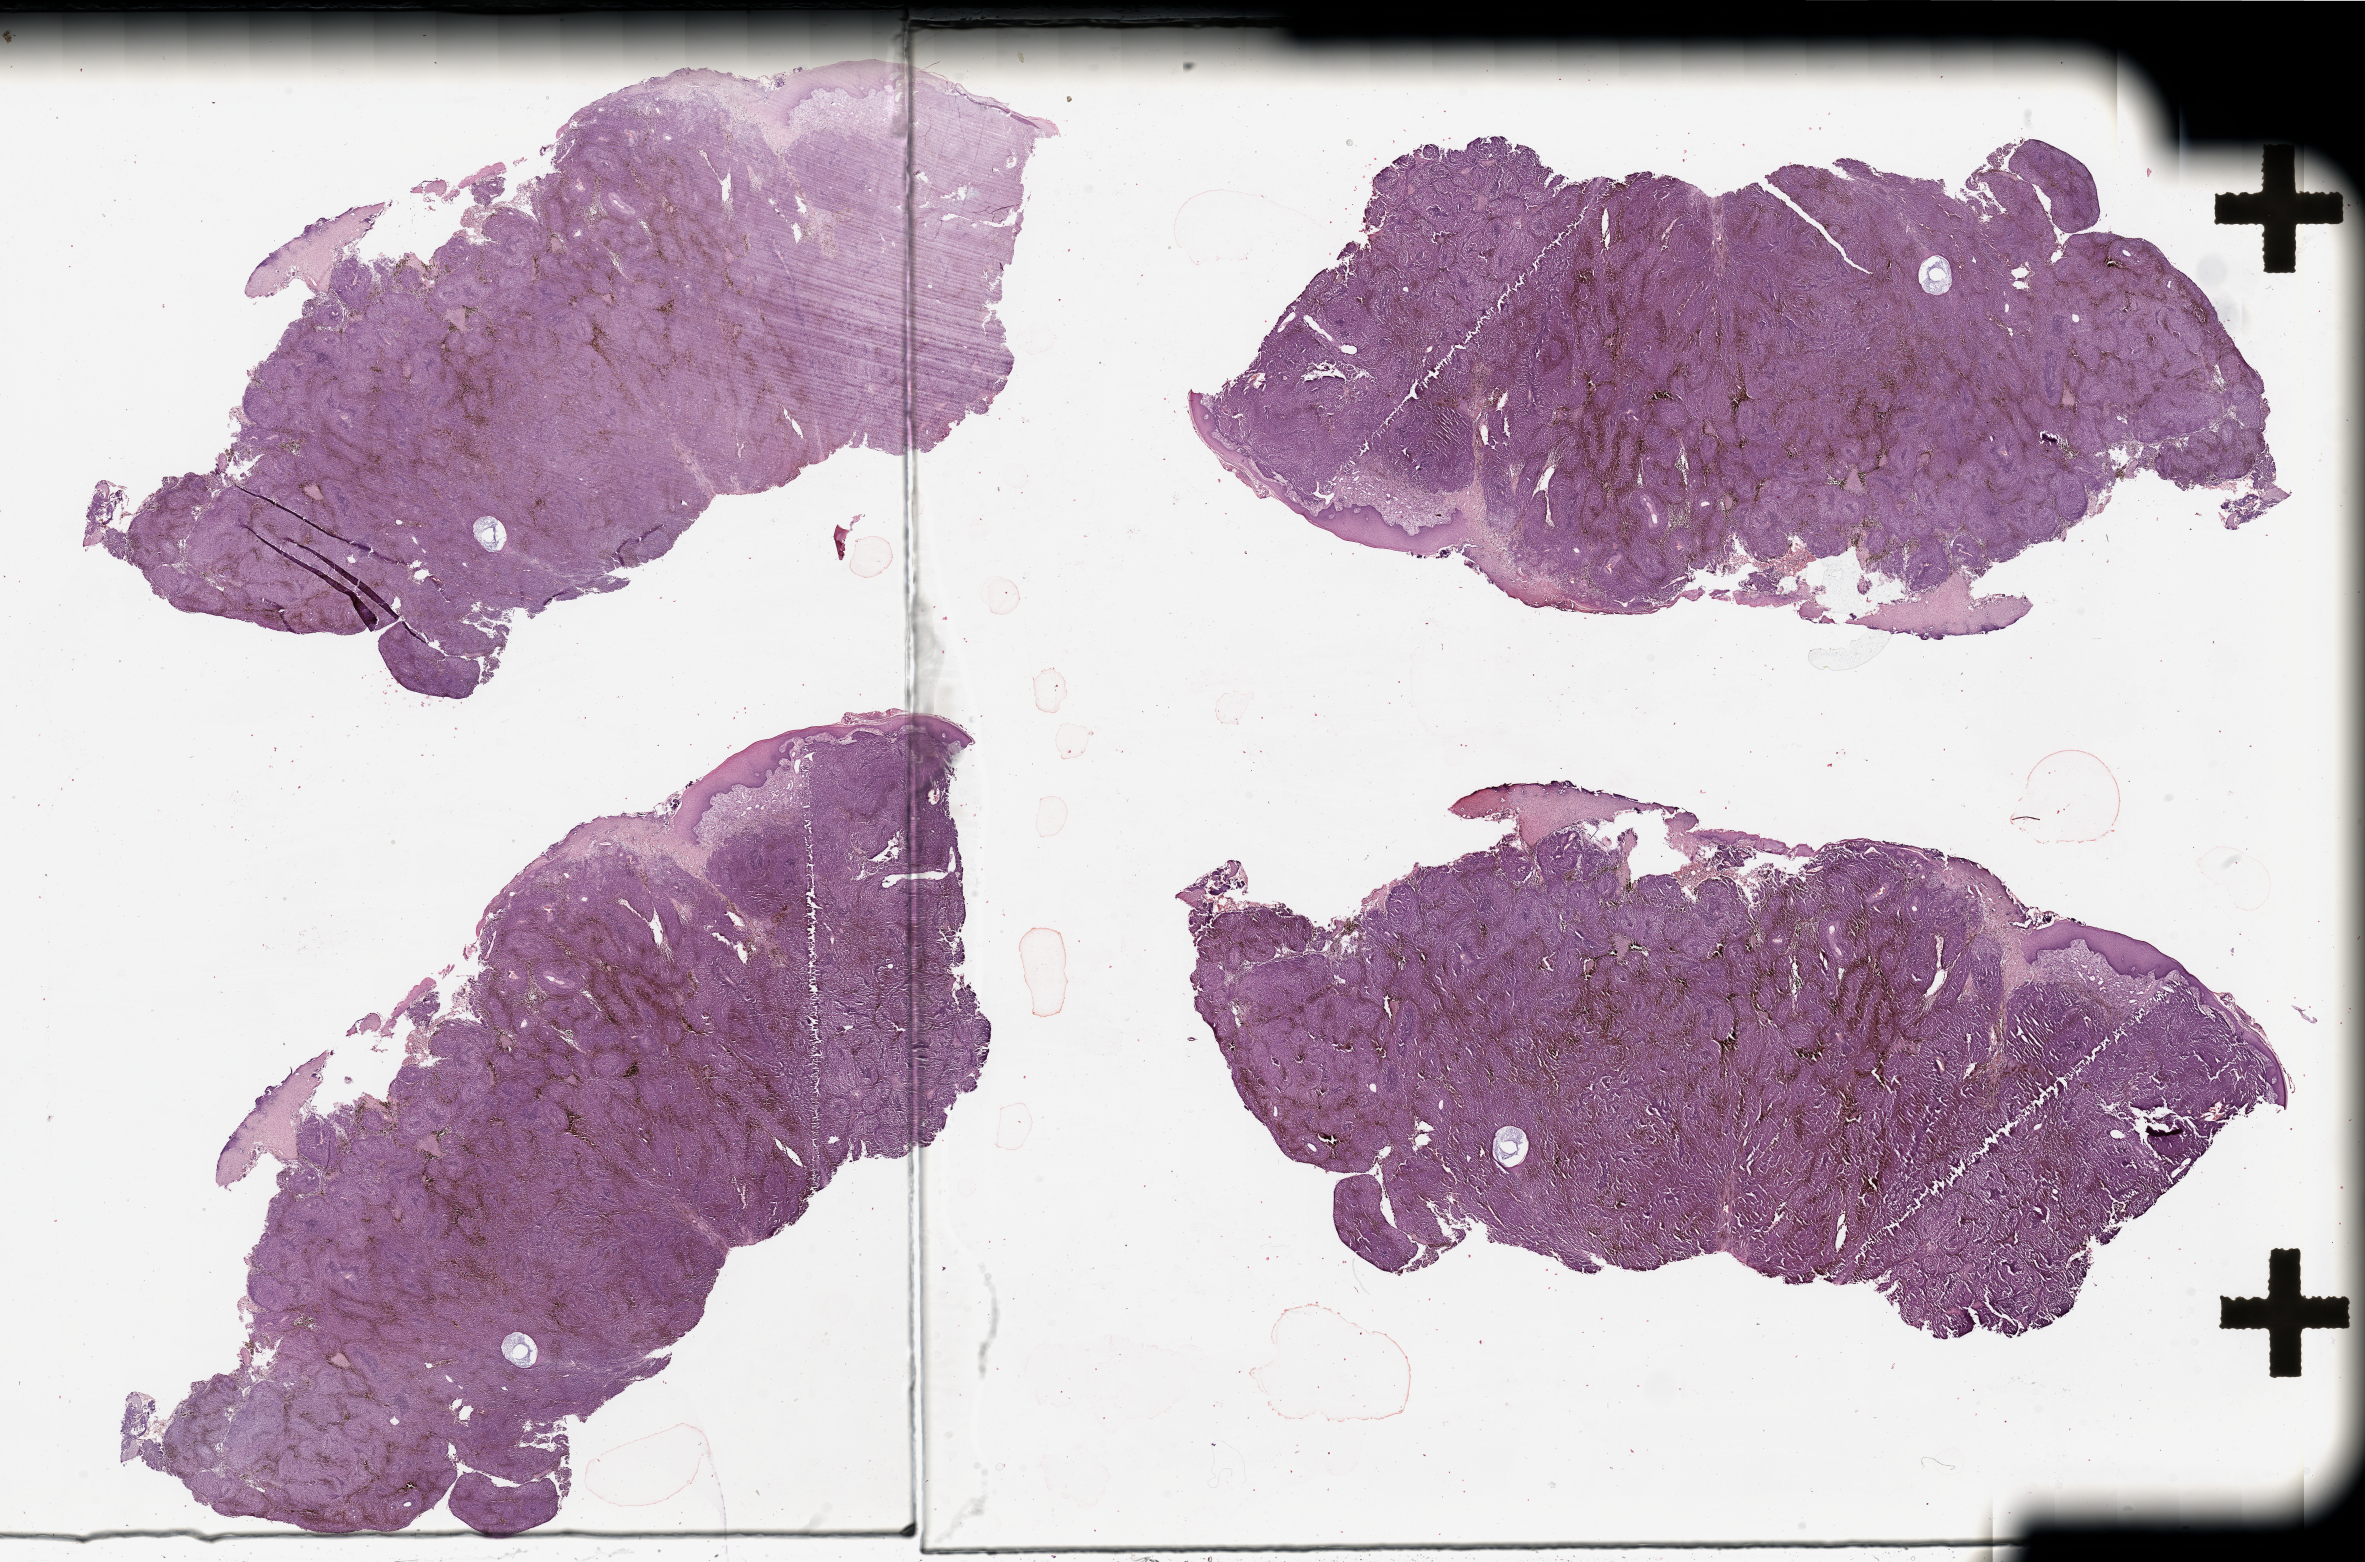
H&E whole-slide image — a low-resolution overview of the entire scanned area, about 37.4 x 24.7 mm (slide scanned at 20x); melanoma tumour tissue; sampled site not recorded. Male, 60 y/o.
Primary tumour site (as recorded): trunk. Diagnosis: Malignant melanoma, NOS.